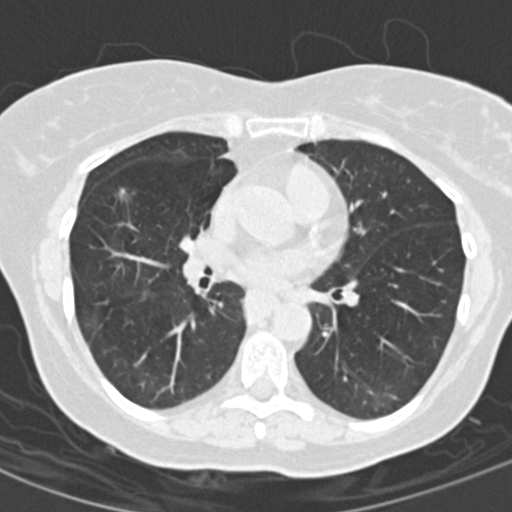
Low-dose screening chest CT, one axial slice; slice 75 of 154 in the series (ordered by position); reconstruction kernel B30f; 120 kVp; lung window (W 1500 / L -600 HU); 2 mm slice thickness; 512 × 512 image matrix, field of view 280 × 280 mm.
Structures marked on this image (expert manual segmentation):
- lesion 2 (nodule, middle lobe of right lung): box from (x=116, y=187) to (x=128, y=202) px